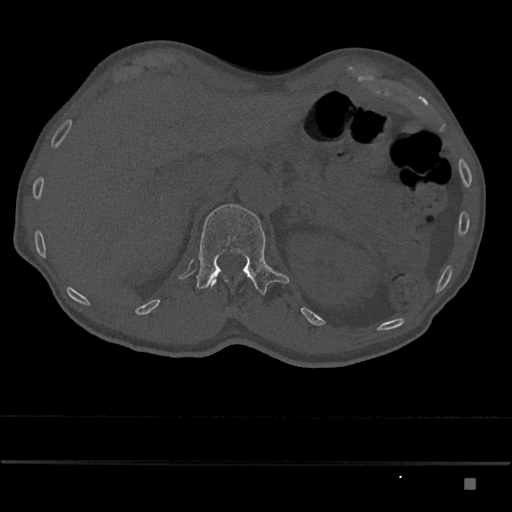
CT including the spine, one axial slice; slice 561 of 797 in the series (ordered by position); reconstruction kernel Br40s/3; 120 kVp; bone window (W 1800 / L 400 HU); 0.5 mm slice thickness; 512 × 512 image matrix, field of view 390 × 390 mm. Patient: male, 72 years. Case-level facts recorded for this patient, not image findings: primary cancer: prostate.
Structures marked on this image (semi-automatically segmented with operator editing):
- L1 vertebra: bounding box <196,204,290,294> (left, top, right, bottom; pixels)
- T12 vertebra: <209,277,228,287>